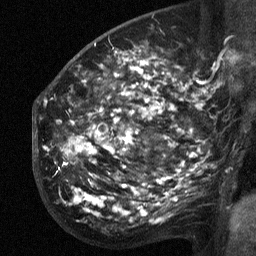
Breast MRI (dynamic contrast-enhanced), one sagittal slice; slice 37 of 64 in the series (ordered by position); dynamic contrast-enhanced study with each time point stored as its own series, time point 2 of 3 at this slice position (early post-contrast, ordered by acquisition time); 1.5 T; TE 4.8 ms, TR 27 ms; 2.3 mm slice thickness; 256 × 256 image matrix, field of view 200 × 200 mm. Female patient, age 50 years. From the clinical record (not read from this slice): setting: breast cancer imaged before/during neoadjuvant chemotherapy; receptor status: HER2-positive.
Annotated regions visible in this slice (semi-automatically segmented with operator editing):
- analysis volume of interest (the breast-tissue region the enhancement analysis was run in; not a lesion): bounding box (x1, y1, x2, y2) in pixels: (53, 64, 211, 218)
- tumour enhancement mask (voxels above the 90 % enhancement threshold inside the analysis volume of interest): (65, 64, 202, 212)